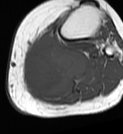
MRI of an extremity soft-tissue mass, one axial slice. Slice 38 of 68 in the series (ordered by position). MR volume resampled by the dataset authors to the PET/CT grid (not the native acquisition matrix). 123 × 134 image matrix. Female patient. Case-level facts recorded for this patient, not image findings: histological type: extraskeletal high grade osteogenic sarcoma; grade: high; site of the primary tumour: left calf.
Outlined on this slice (expert contour drawn on MRI and transferred to this co-registered scan by the dataset authors):
- gross tumour volume (mass): bounding box (x1, y1, x2, y2) in pixels: (22, 32, 87, 95)